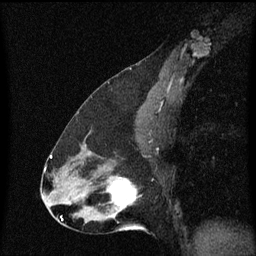
Breast MRI (dynamic contrast-enhanced), one sagittal slice; slice 35 of 60 in the series (ordered by position); dynamic contrast-enhanced series, image 2 of 3 at this slice position (ordered by acquisition); 1.5 T; TE 4.2 ms, TR 8.4 ms; 256 × 256 image matrix, field of view 200 × 200 mm. Female patient, age 47 years.
Outlined on this slice (semi-automatic segmentation, software-assisted and operator-edited):
- analysis volume of interest (the breast-tissue region the enhancement analysis was run in; not a lesion): bounding box <100,172,139,219> (left, top, right, bottom; pixels)
- tumour enhancement mask (voxels above the 70 % enhancement threshold inside the analysis volume of interest): <108,178,138,211>